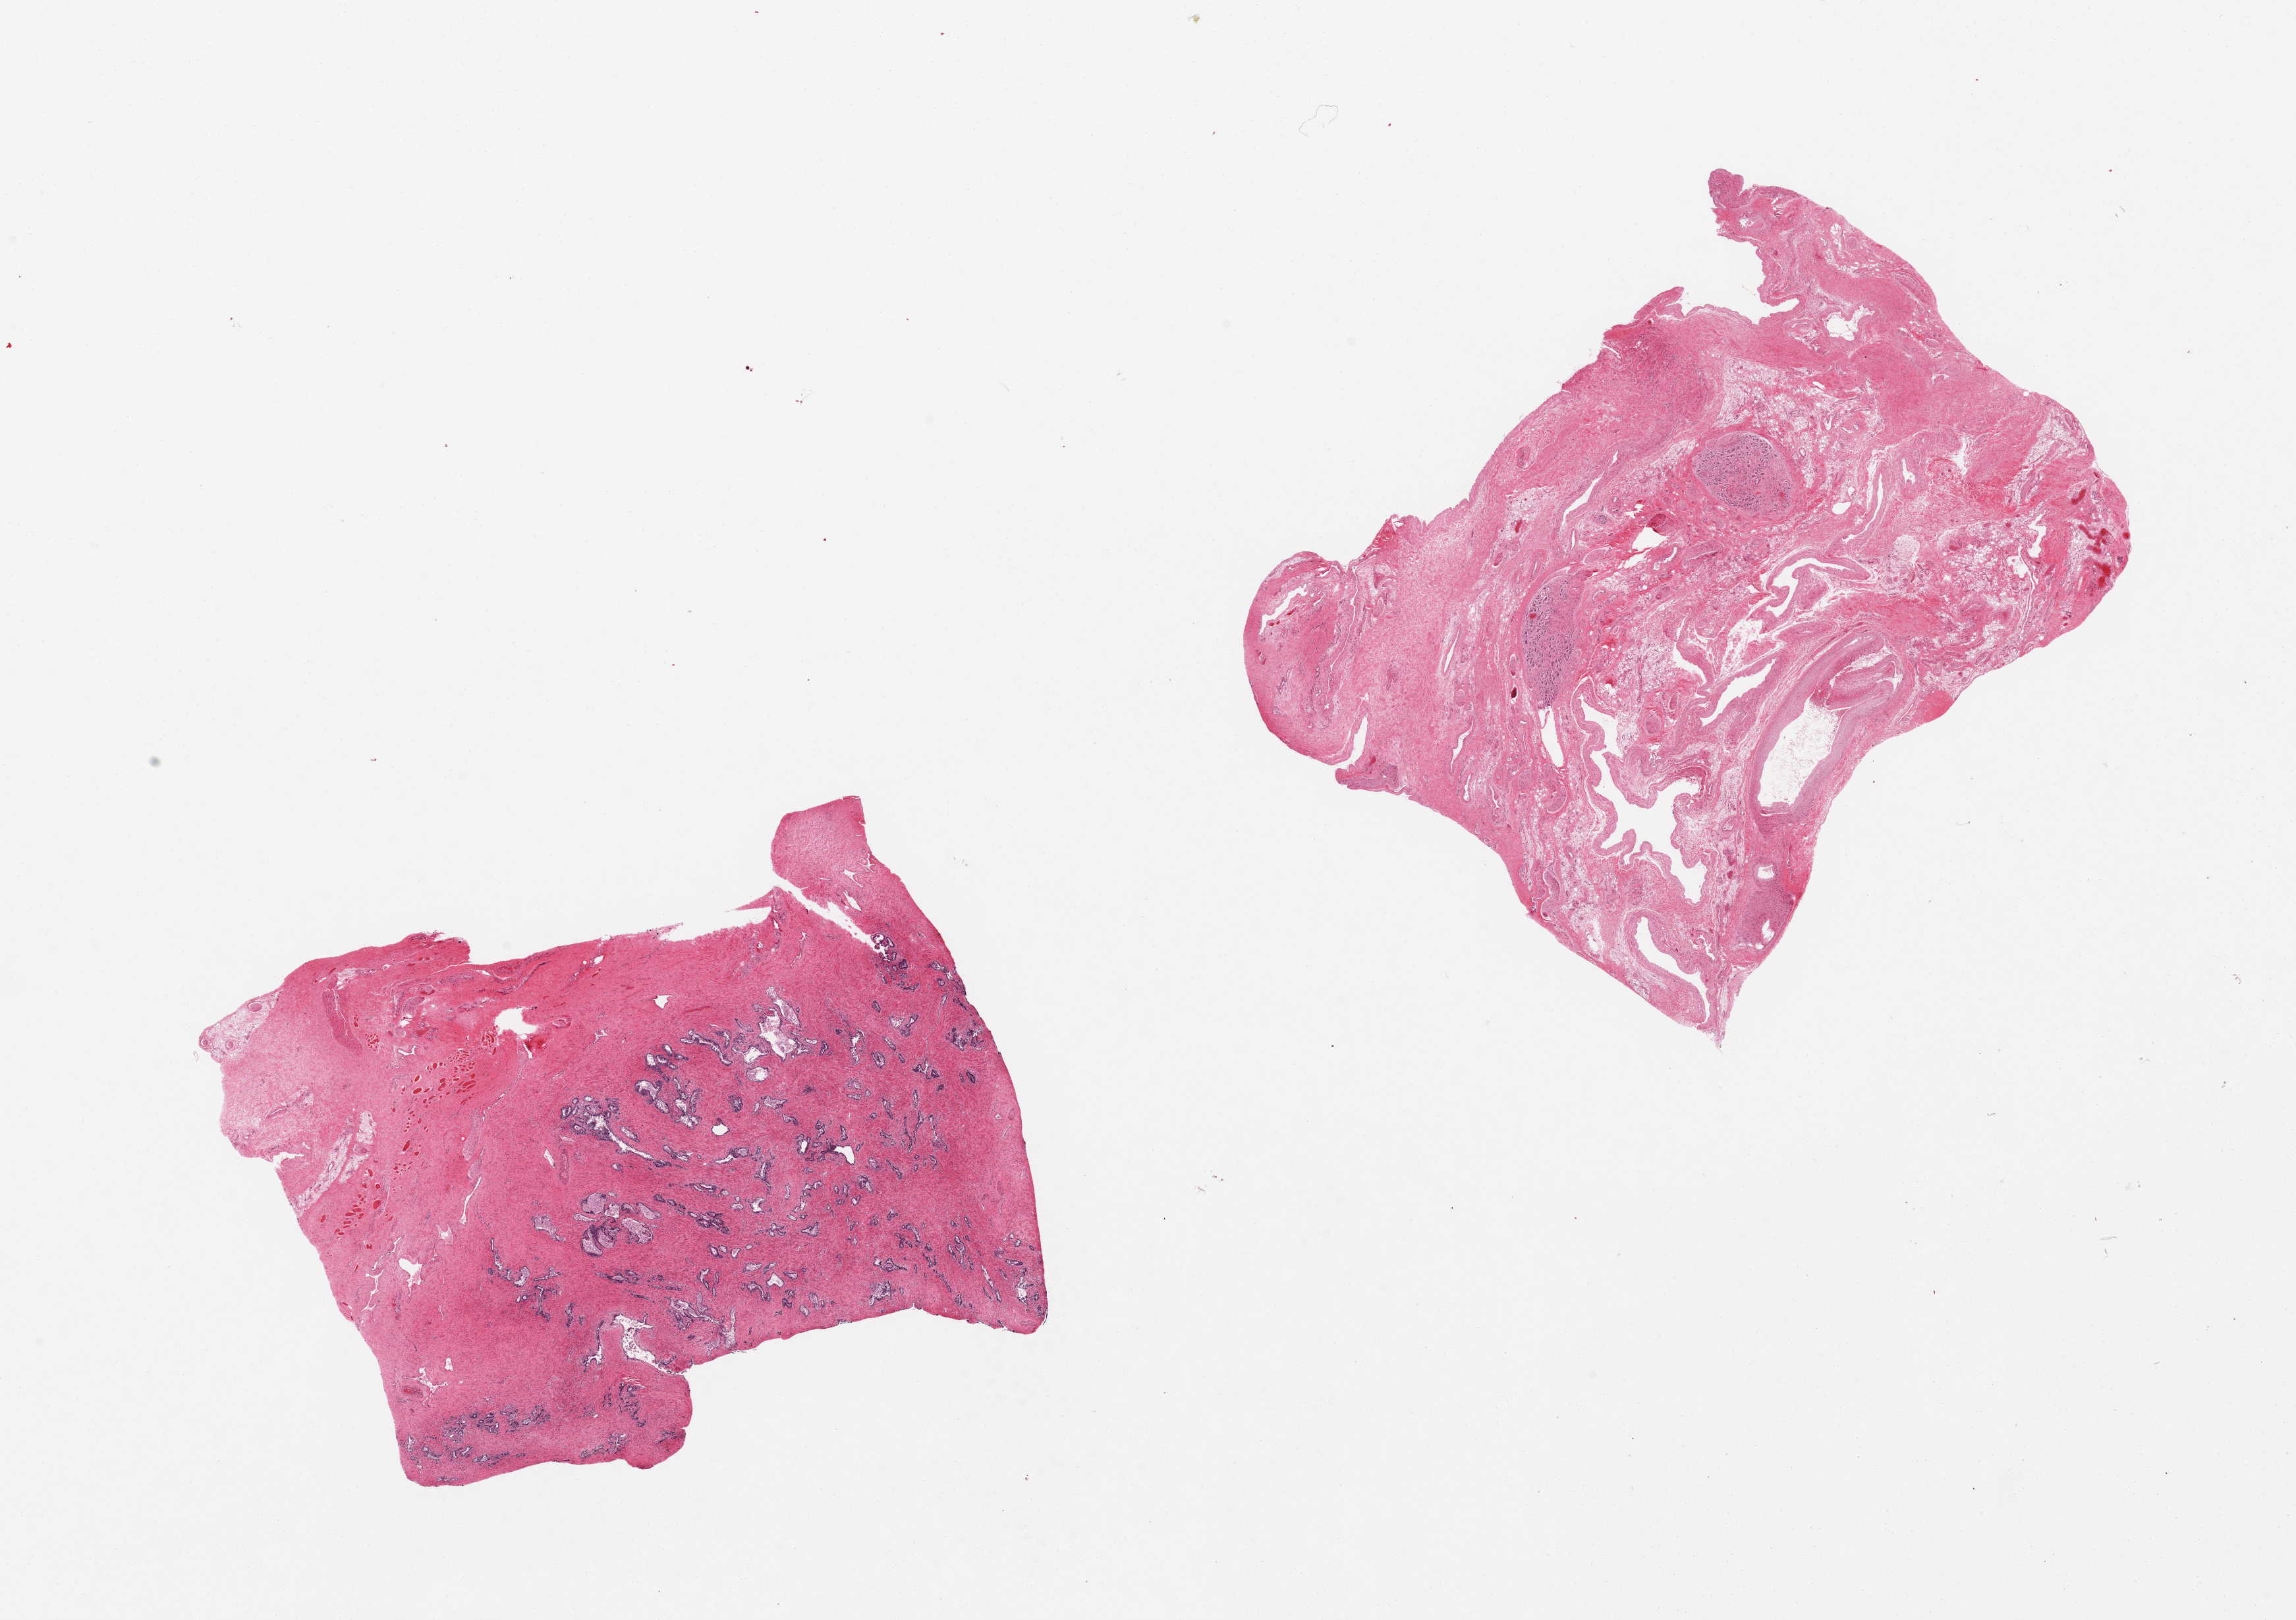
Digitized H&E-stained section, whole scanned area (about 27.6 x 19.4 mm, acquisition: 20x scan) shown as a low-resolution overview. PAXgene-fixed, paraffin-embedded tissue. Sampled site (target tissue): prostate. Donor tissue sample.
Pathologist's review note for this sample: 2 pieces, one is largely stroma/peripheral connective tissue; glandular elements in other moderately autolzyed.